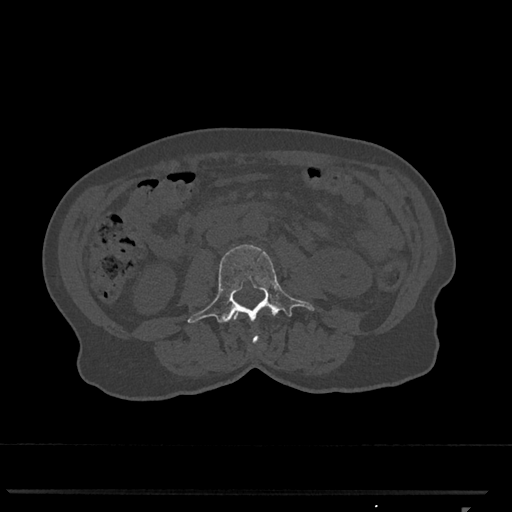
CT including the spine, one axial slice. Slice 282 of 793 in the series (ordered by position). 120 kVp. Bone window (W 1800 / L 400 HU). 512 × 512 image matrix, field of view 380 × 380 mm. Female patient, age 62 years. From the clinical record (not read from this slice): primary cancer: renal.
Structures marked on this image (semi-automatically segmented with operator editing):
- L2 vertebra: bounding box (x1, y1, x2, y2) in pixels: (233, 312, 260, 344)
- L3 vertebra: (187, 244, 315, 323)